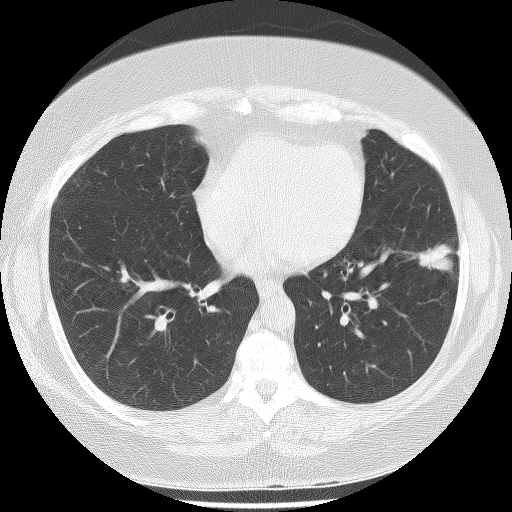
Low-dose screening chest CT, one axial slice; slice 106 of 233 in the series (ordered by position); reconstruction kernel BONE; lung window (W 1500 / L -600 HU); 2.5 mm slice thickness; 512 × 512 image matrix, field of view 340 × 340 mm.
Outlined on this slice (expert manual segmentation):
- lesion 1 (tumor, lower lobe of left lung): box from (x=414, y=244) to (x=460, y=274) px